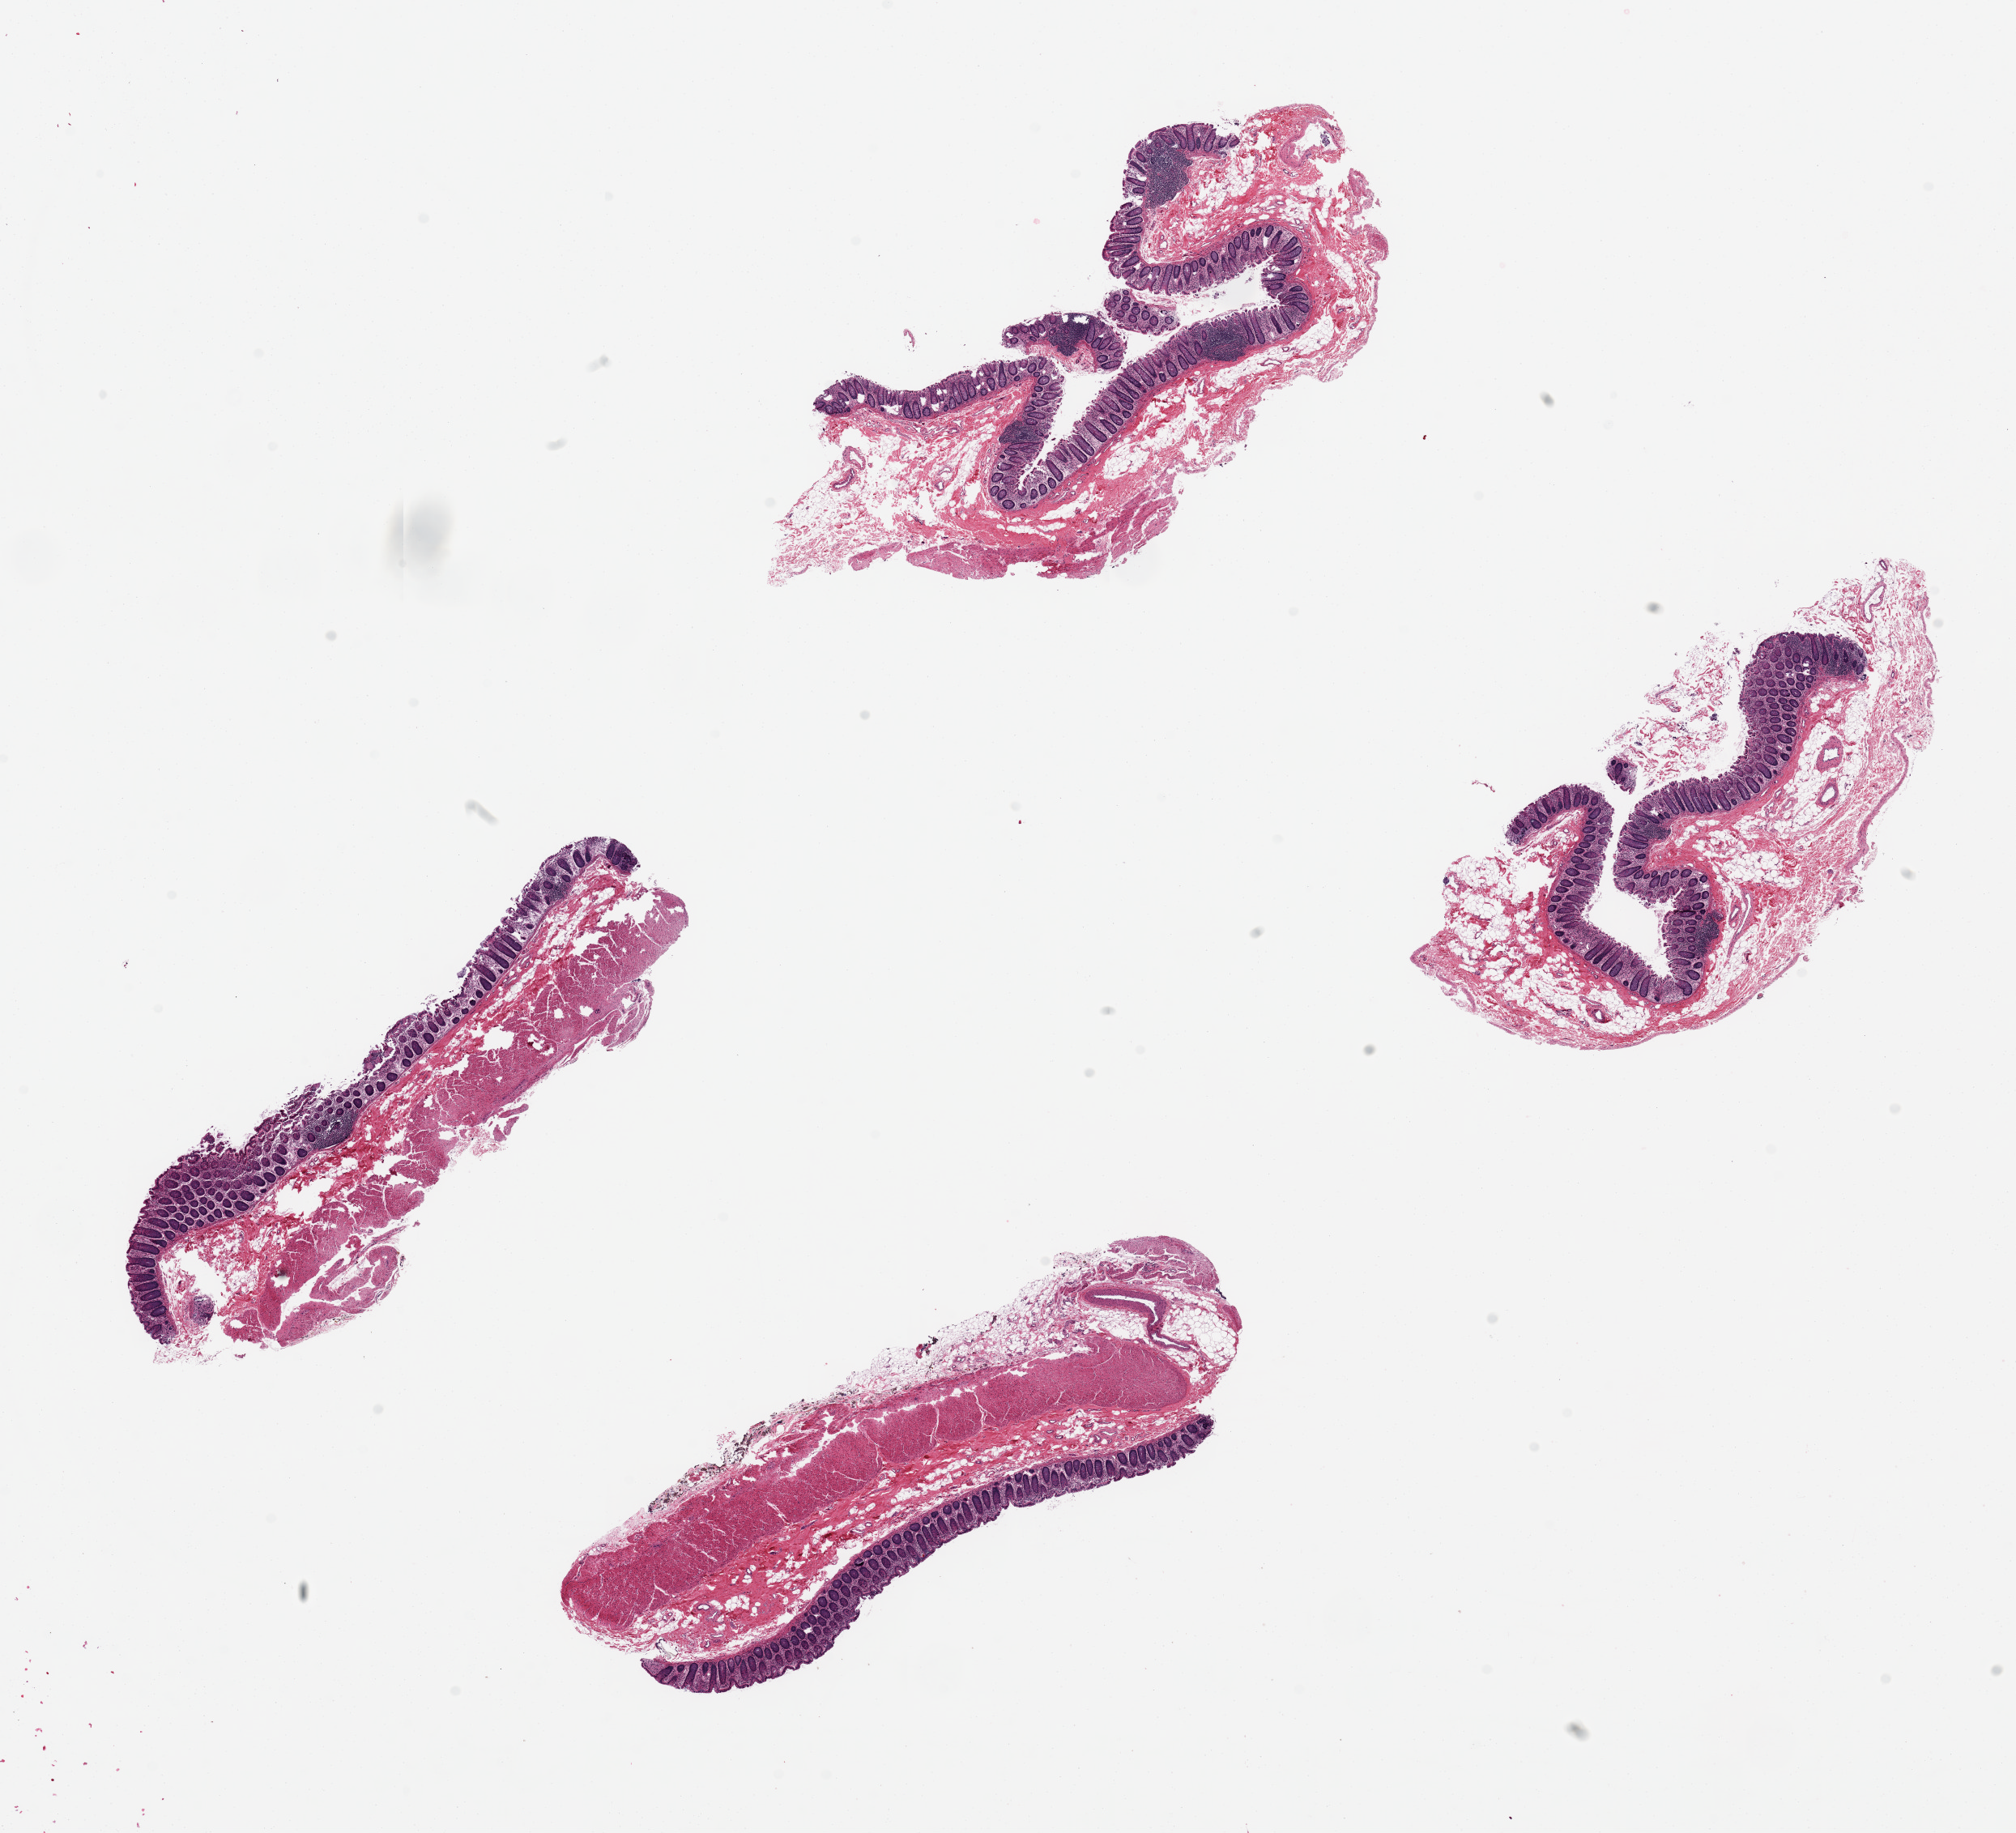
Whole-slide image, H&E stain — whole scanned area (about 19.7 x 17.9 mm, acquisition: 20x scan) shown as a low-resolution overview. PAXgene-fixed paraffin-embedded (PFPE) section. Sampled site (target tissue): transverse colon. Tissue donor sample. Donor: male.
Review note (as recorded): 4 pieces, 7x2mm. Good mucosal preservation. Tissue separation with tears.